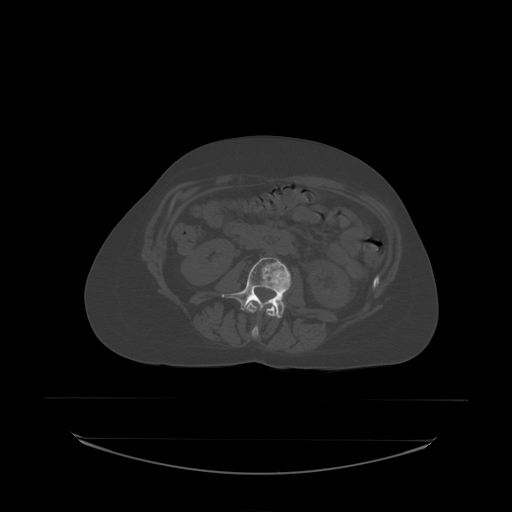
CT including the spine, one axial slice; position 64 of 242 along the scan axis; bone window (W 1800 / L 400 HU); 2.5 mm slice thickness; 512 × 512 image matrix, field of view 500 × 500 mm. Female patient, age 53 years. Case-level facts recorded for this patient, not image findings: primary cancer: lung; vertebrae with lytic lesions (as recorded): T7, L1.
Annotated regions visible in this slice (semi-automatically segmented with operator editing):
- L2 vertebra: box from (x=247, y=303) to (x=280, y=338) px
- L3 vertebra: (x=222, y=258)–(x=292, y=318)